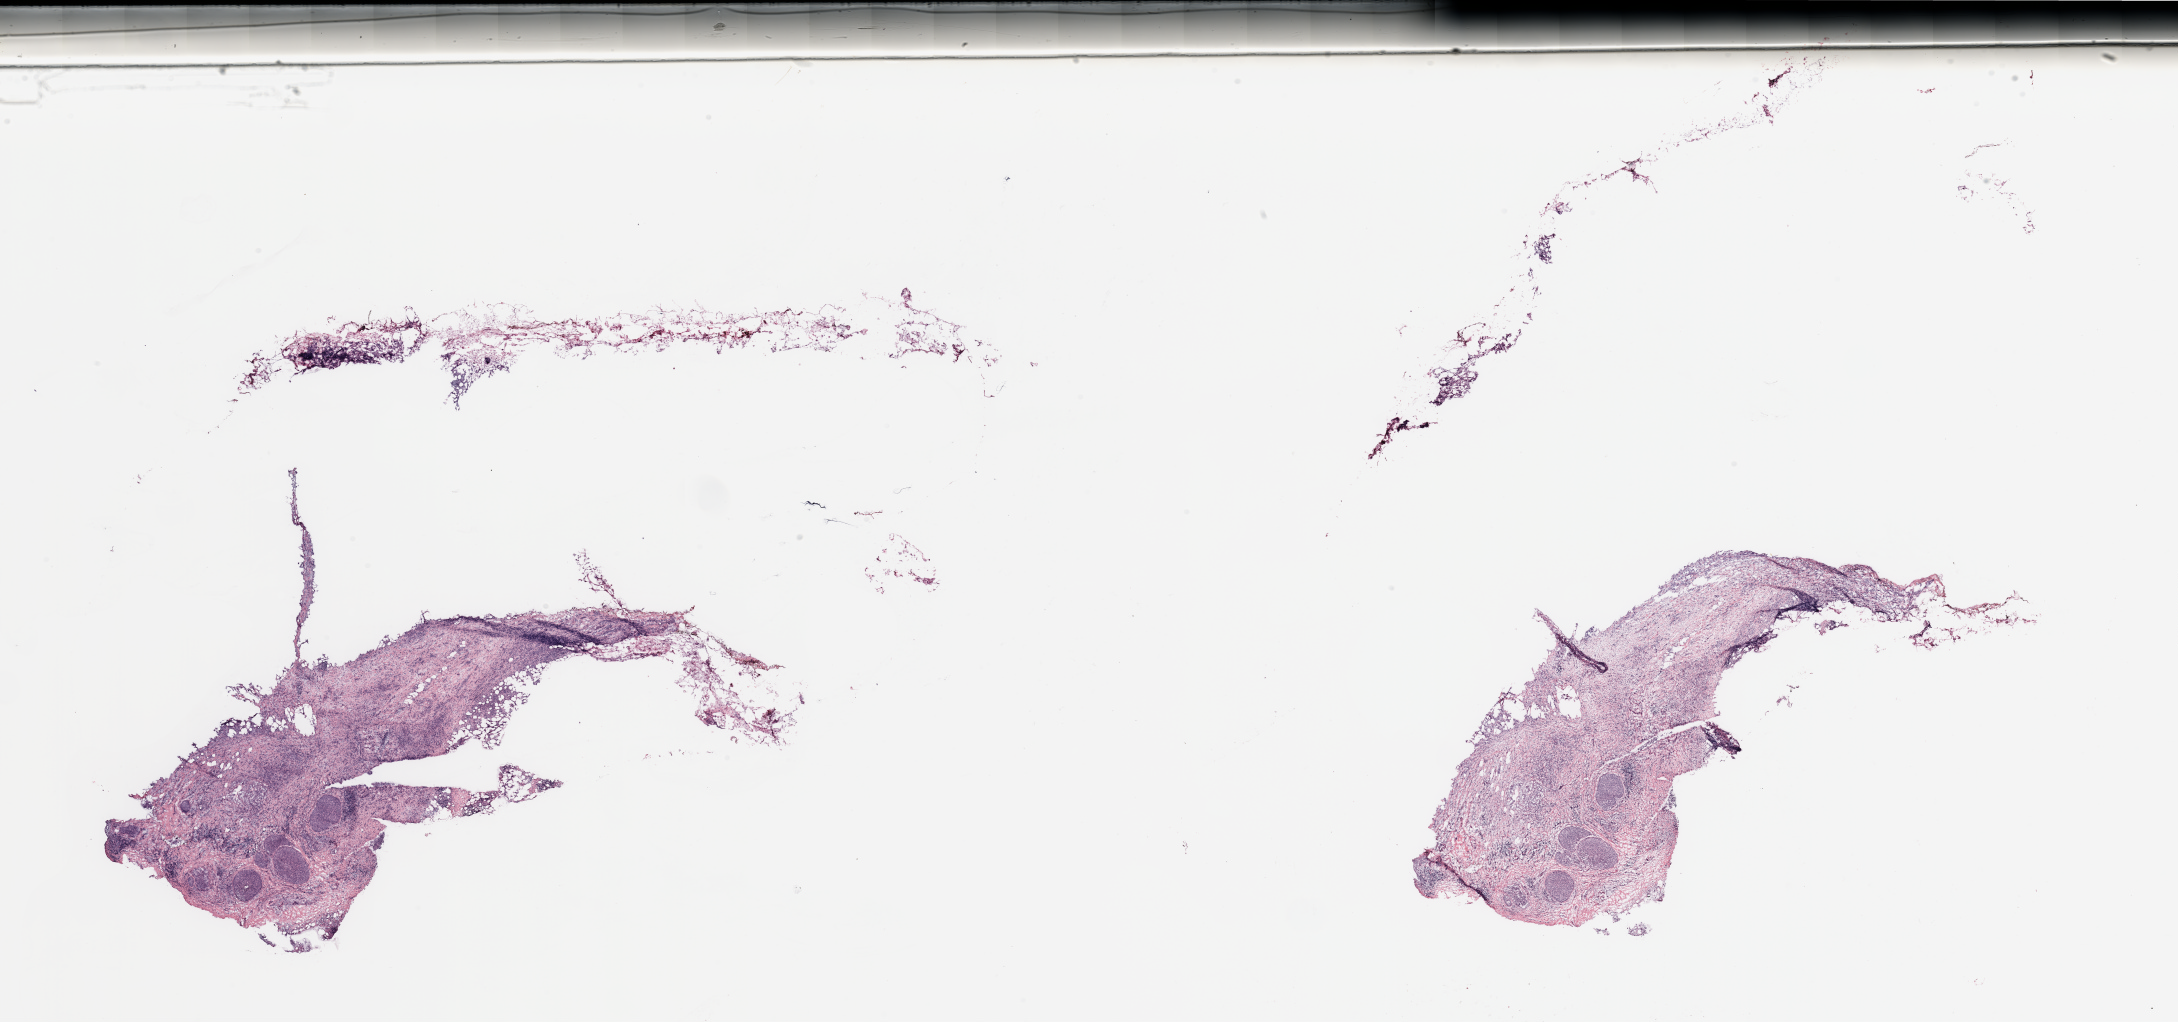
Whole-slide histology image, H&E-stained, a low-resolution overview of the entire scanned area, about 34.5 x 16.2 mm (acquisition: 20x scan). Breast, tissue type not recorded.
Patient diagnosis (cohort enrolment): breast cancer (breast).